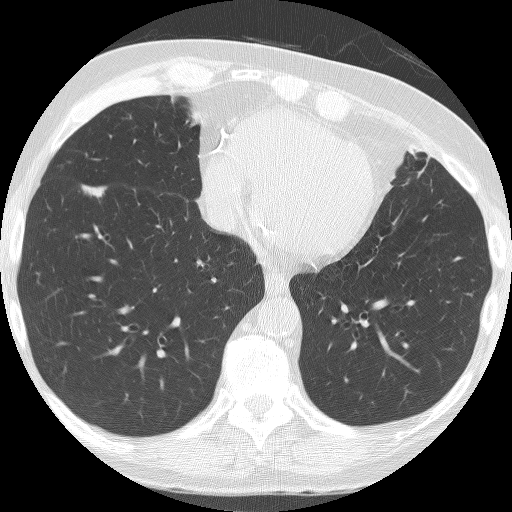
Low-dose screening chest CT, axial slice; first (baseline) screen; lung window (W 1500 / L -600 HU); lung (sharp) reconstruction kernel (BONE); slice 112 of 182 in the series. Male participant, aged 74 years at enrolment.
- Lesion marked by an expert reader, bounding box (x1, y1, x2, y2) in pixels: (73, 172, 118, 208).
- The screening reader recorded 4 non-calcified nodules or masses ≥4 mm on this exam; which of them this box marks is not recorded.
- Later outcome: lung cancer diagnosed 35 days after this screen — bronchiolo-alveolar carcinoma, mucinous, right lower lobe, well differentiated (G1), stage IA (AJCC 6th edition), 22 mm at pathology.